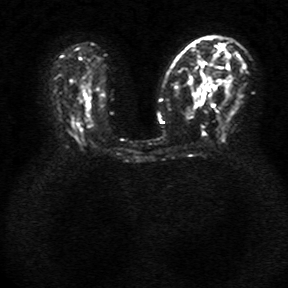
Breast MRI, one axial slice. Position 17 of 34 along the scan axis. Diffusion-weighted series; image 2 of 4 stored at this slice position (different b-values; order by instance number). 1.5 T. 288 × 288 image matrix, field of view 340 × 340 mm. Female patient.
Outlined on this slice (manually delineated by an expert):
- tumour on diffusion-weighted imaging: bounding box (x1, y1, x2, y2) in pixels: (201, 73, 211, 86)